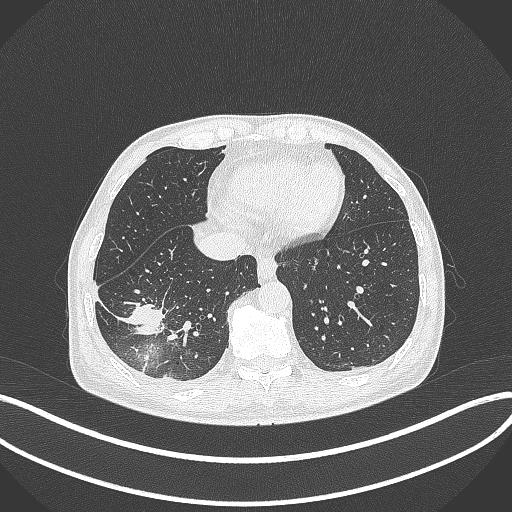
Chest CT, one axial slice; 120 kVp; lung window (W 1500 / L -600 HU); 1 mm slice thickness; 512 × 512 image matrix. Patient: male, 64 years. From the clinical record (not read from this slice): clinical TNM (as recorded): T3 N0 M0; histopathological grade: G2-3.
Outlined on this slice (rectangle marked by the reading radiologist):
- lung tumour (recorded histology: adenocarcinoma): bounding box <119,293,169,339> (left, top, right, bottom; pixels)